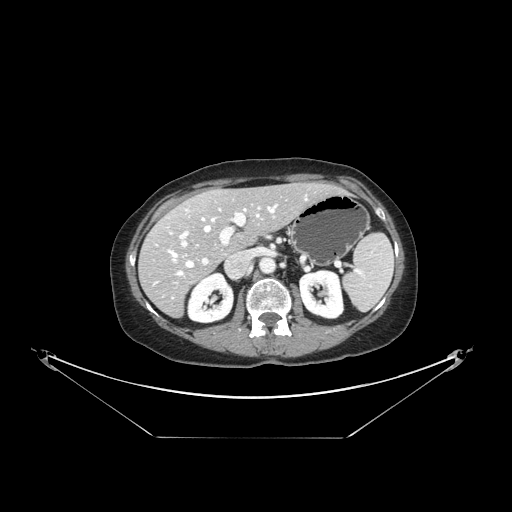
Contrast-enhanced abdominal CT, one axial slice; position 86 of 148 along the scan axis; reconstruction kernel STANDARD; intravenous contrast given; soft-tissue window (W 400 / L 40 HU); 512 × 512 image matrix, field of view 500 × 500 mm. Female patient, age 73 years. Case-level facts recorded for this patient, not image findings: diagnosis: colorectal cancer liver metastases, imaged before liver resection; multiple liver metastases: no; largest metastasis: 1 cm.
Annotated regions visible in this slice (expert manual segmentation):
- hepatic veins: box from (x=168, y=198) to (x=307, y=275) px
- liver: (x=141, y=184)–(x=336, y=316)
- planned liver remnant (the part of the liver to remain after resection): (x=168, y=184)–(x=336, y=253)
- portal vein (with intrahepatic branches): (x=171, y=207)–(x=260, y=265)